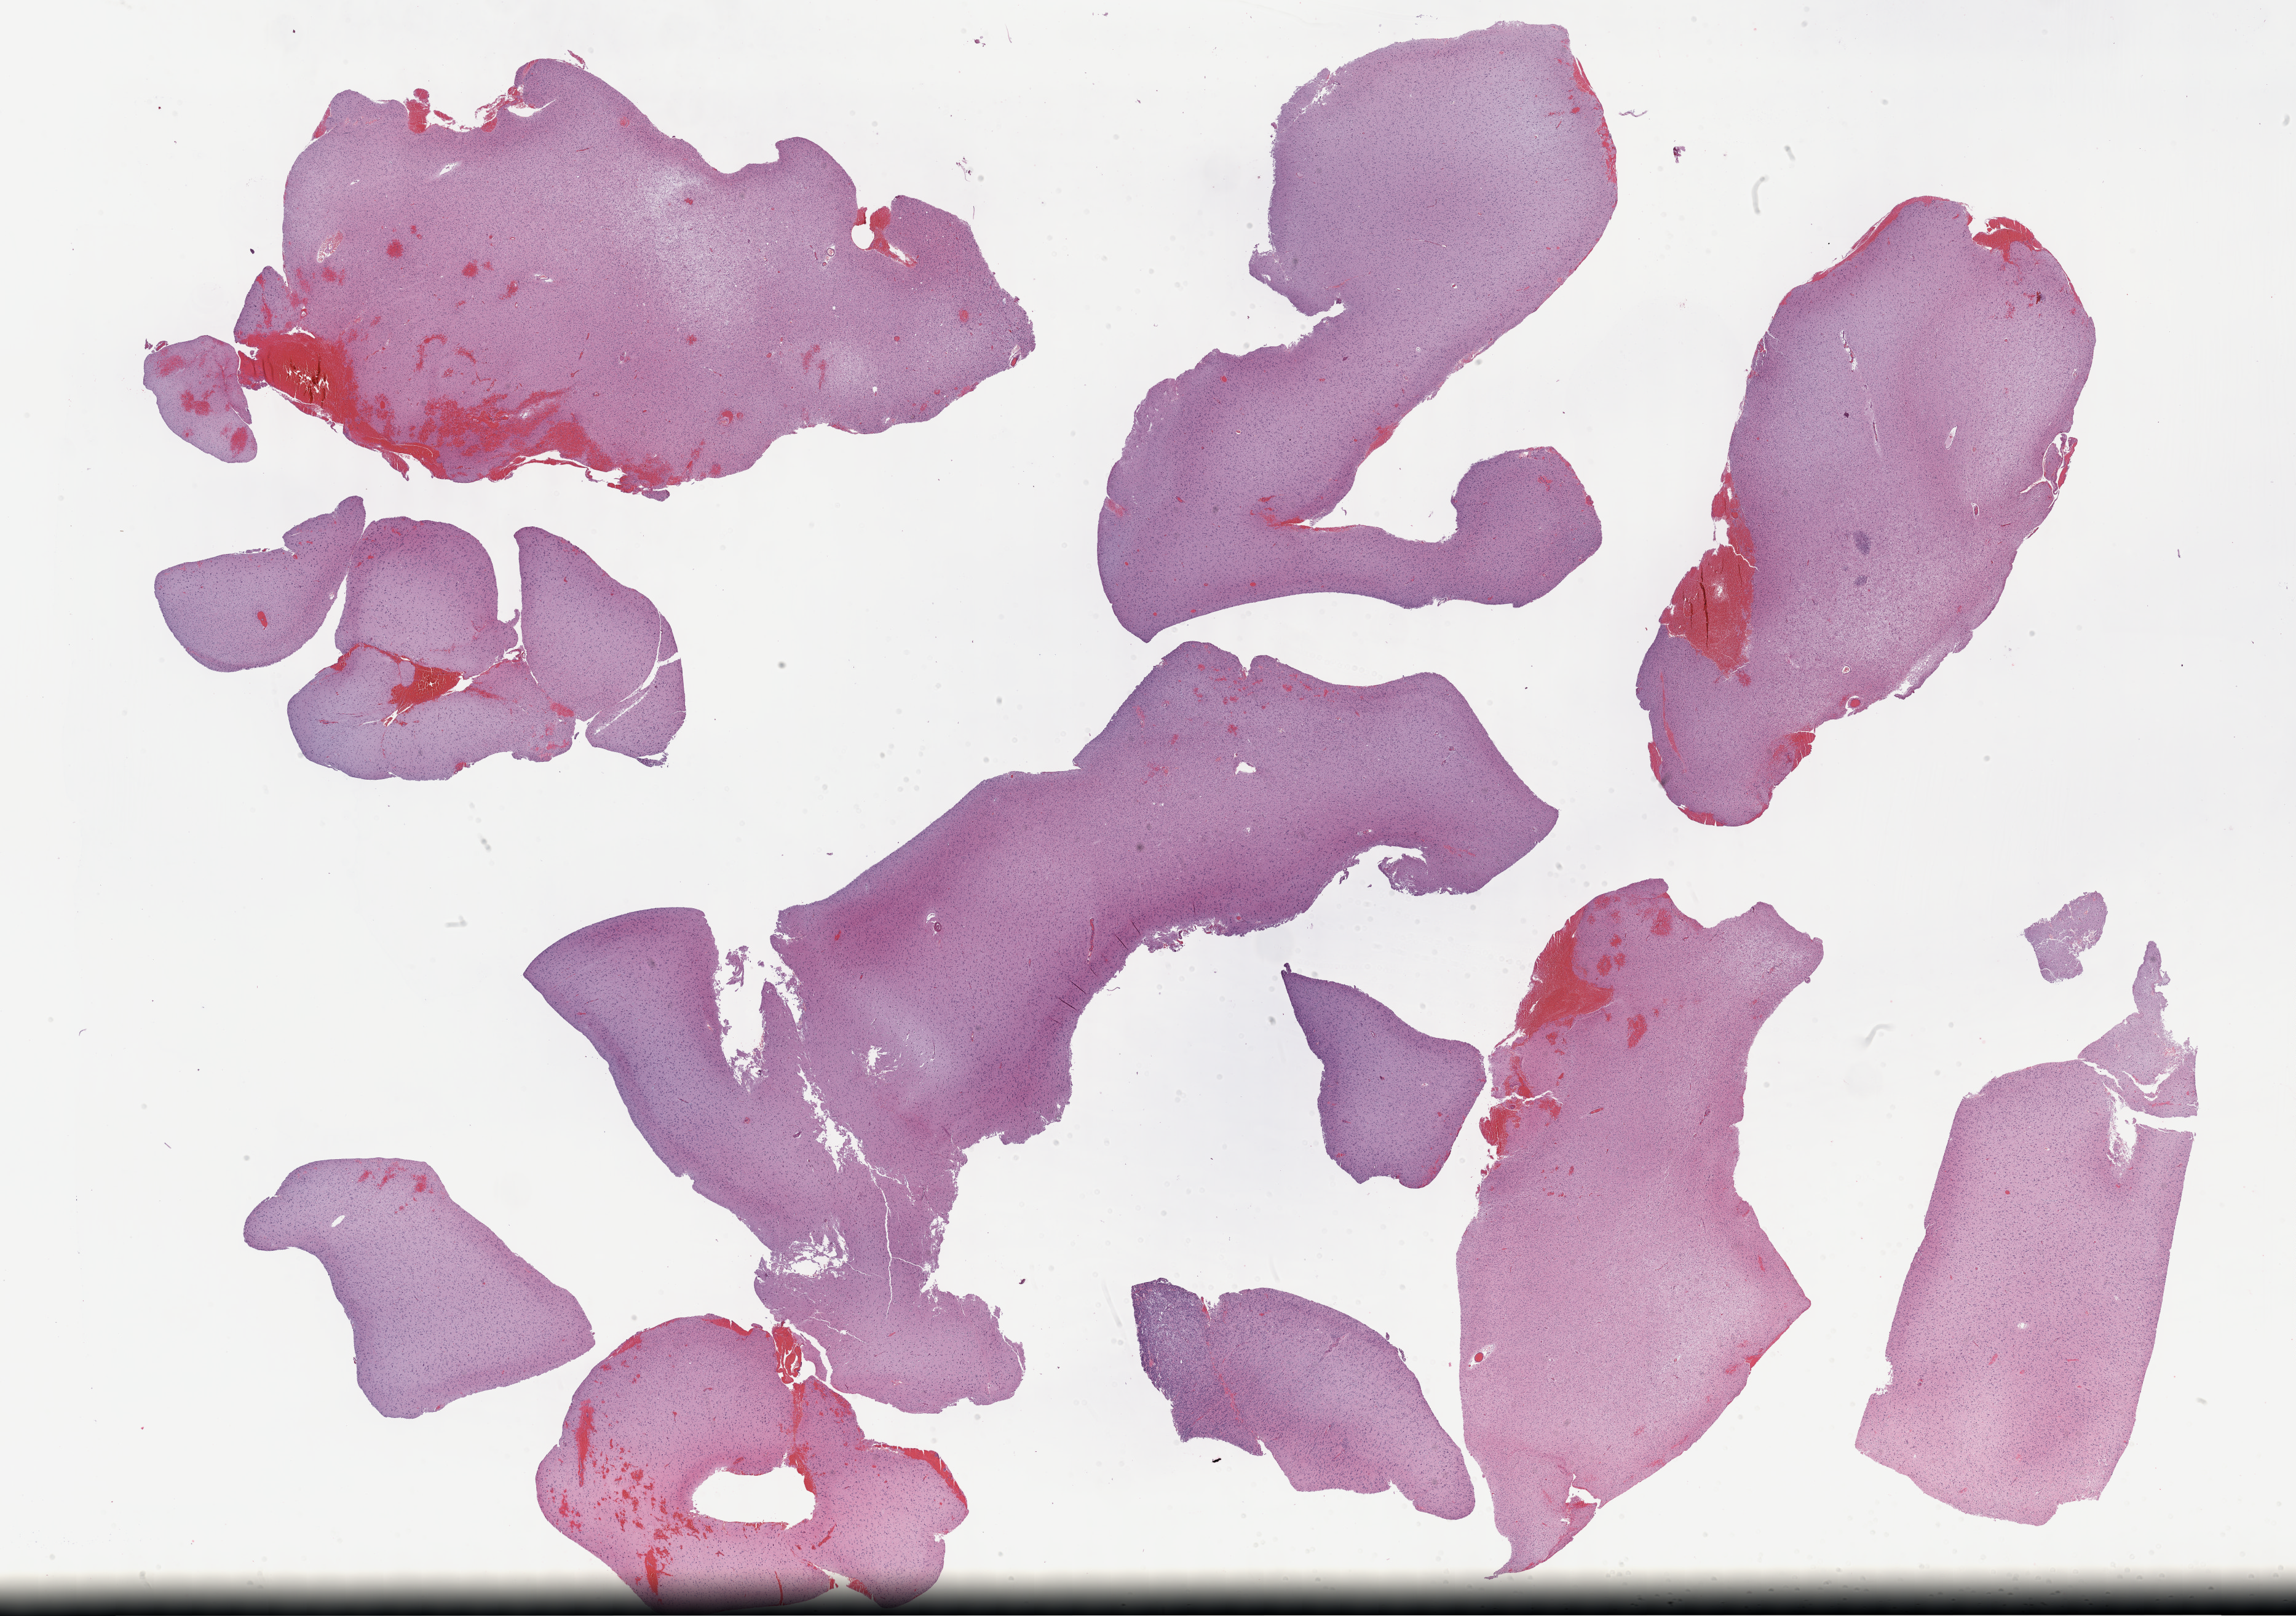
Whole-slide histology image, H&E-stained, a low-resolution overview of the entire scanned area, about 30.2 x 21.3 mm (acquisition: 40x scan), formalin-fixed paraffin-embedded (FFPE) diagnostic section, brain, primary tumour sample. Male patient; age at initial diagnosis 54 years. Histologic grade: G2 (moderately differentiated).
Diagnosis: Oligodendroglioma, NOS (cerebrum).